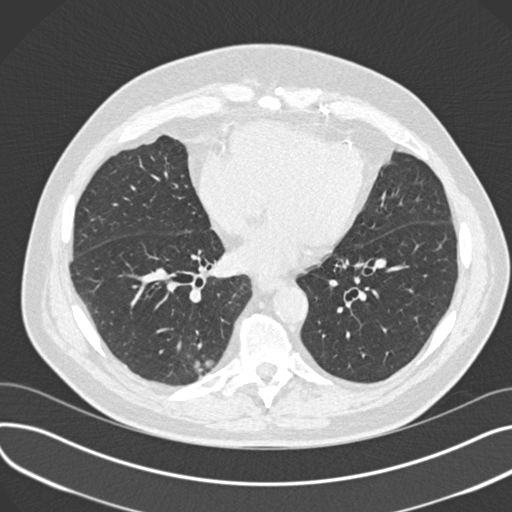
Low-dose screening chest CT, one axial slice; position 73 of 177 along the scan axis; reconstruction kernel B30f; 120 kVp; lung window (W 1500 / L -600 HU); 2 mm slice thickness; 512 × 512 image matrix.
Outlined on this slice (expert manual segmentation):
- lesion 1 (tumor, lower lobe of right lung): bounding box <194,360,214,379> (left, top, right, bottom; pixels)